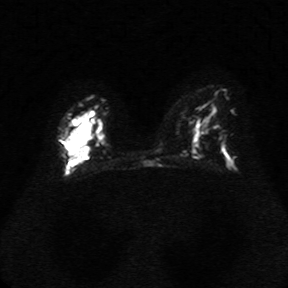
Breast MRI, one axial slice. Slice 21 of 34 in the series (ordered by position). Diffusion-weighted series; image 2 of 4 stored at this slice position (different b-values; order by instance number). 1.5 T. 288 × 288 image matrix, field of view 340 × 340 mm. Female patient.
Outlined on this slice (expert manual segmentation):
- tumour on diffusion-weighted imaging: bounding box [x1, y1, x2, y2] px = [66, 109, 99, 163]